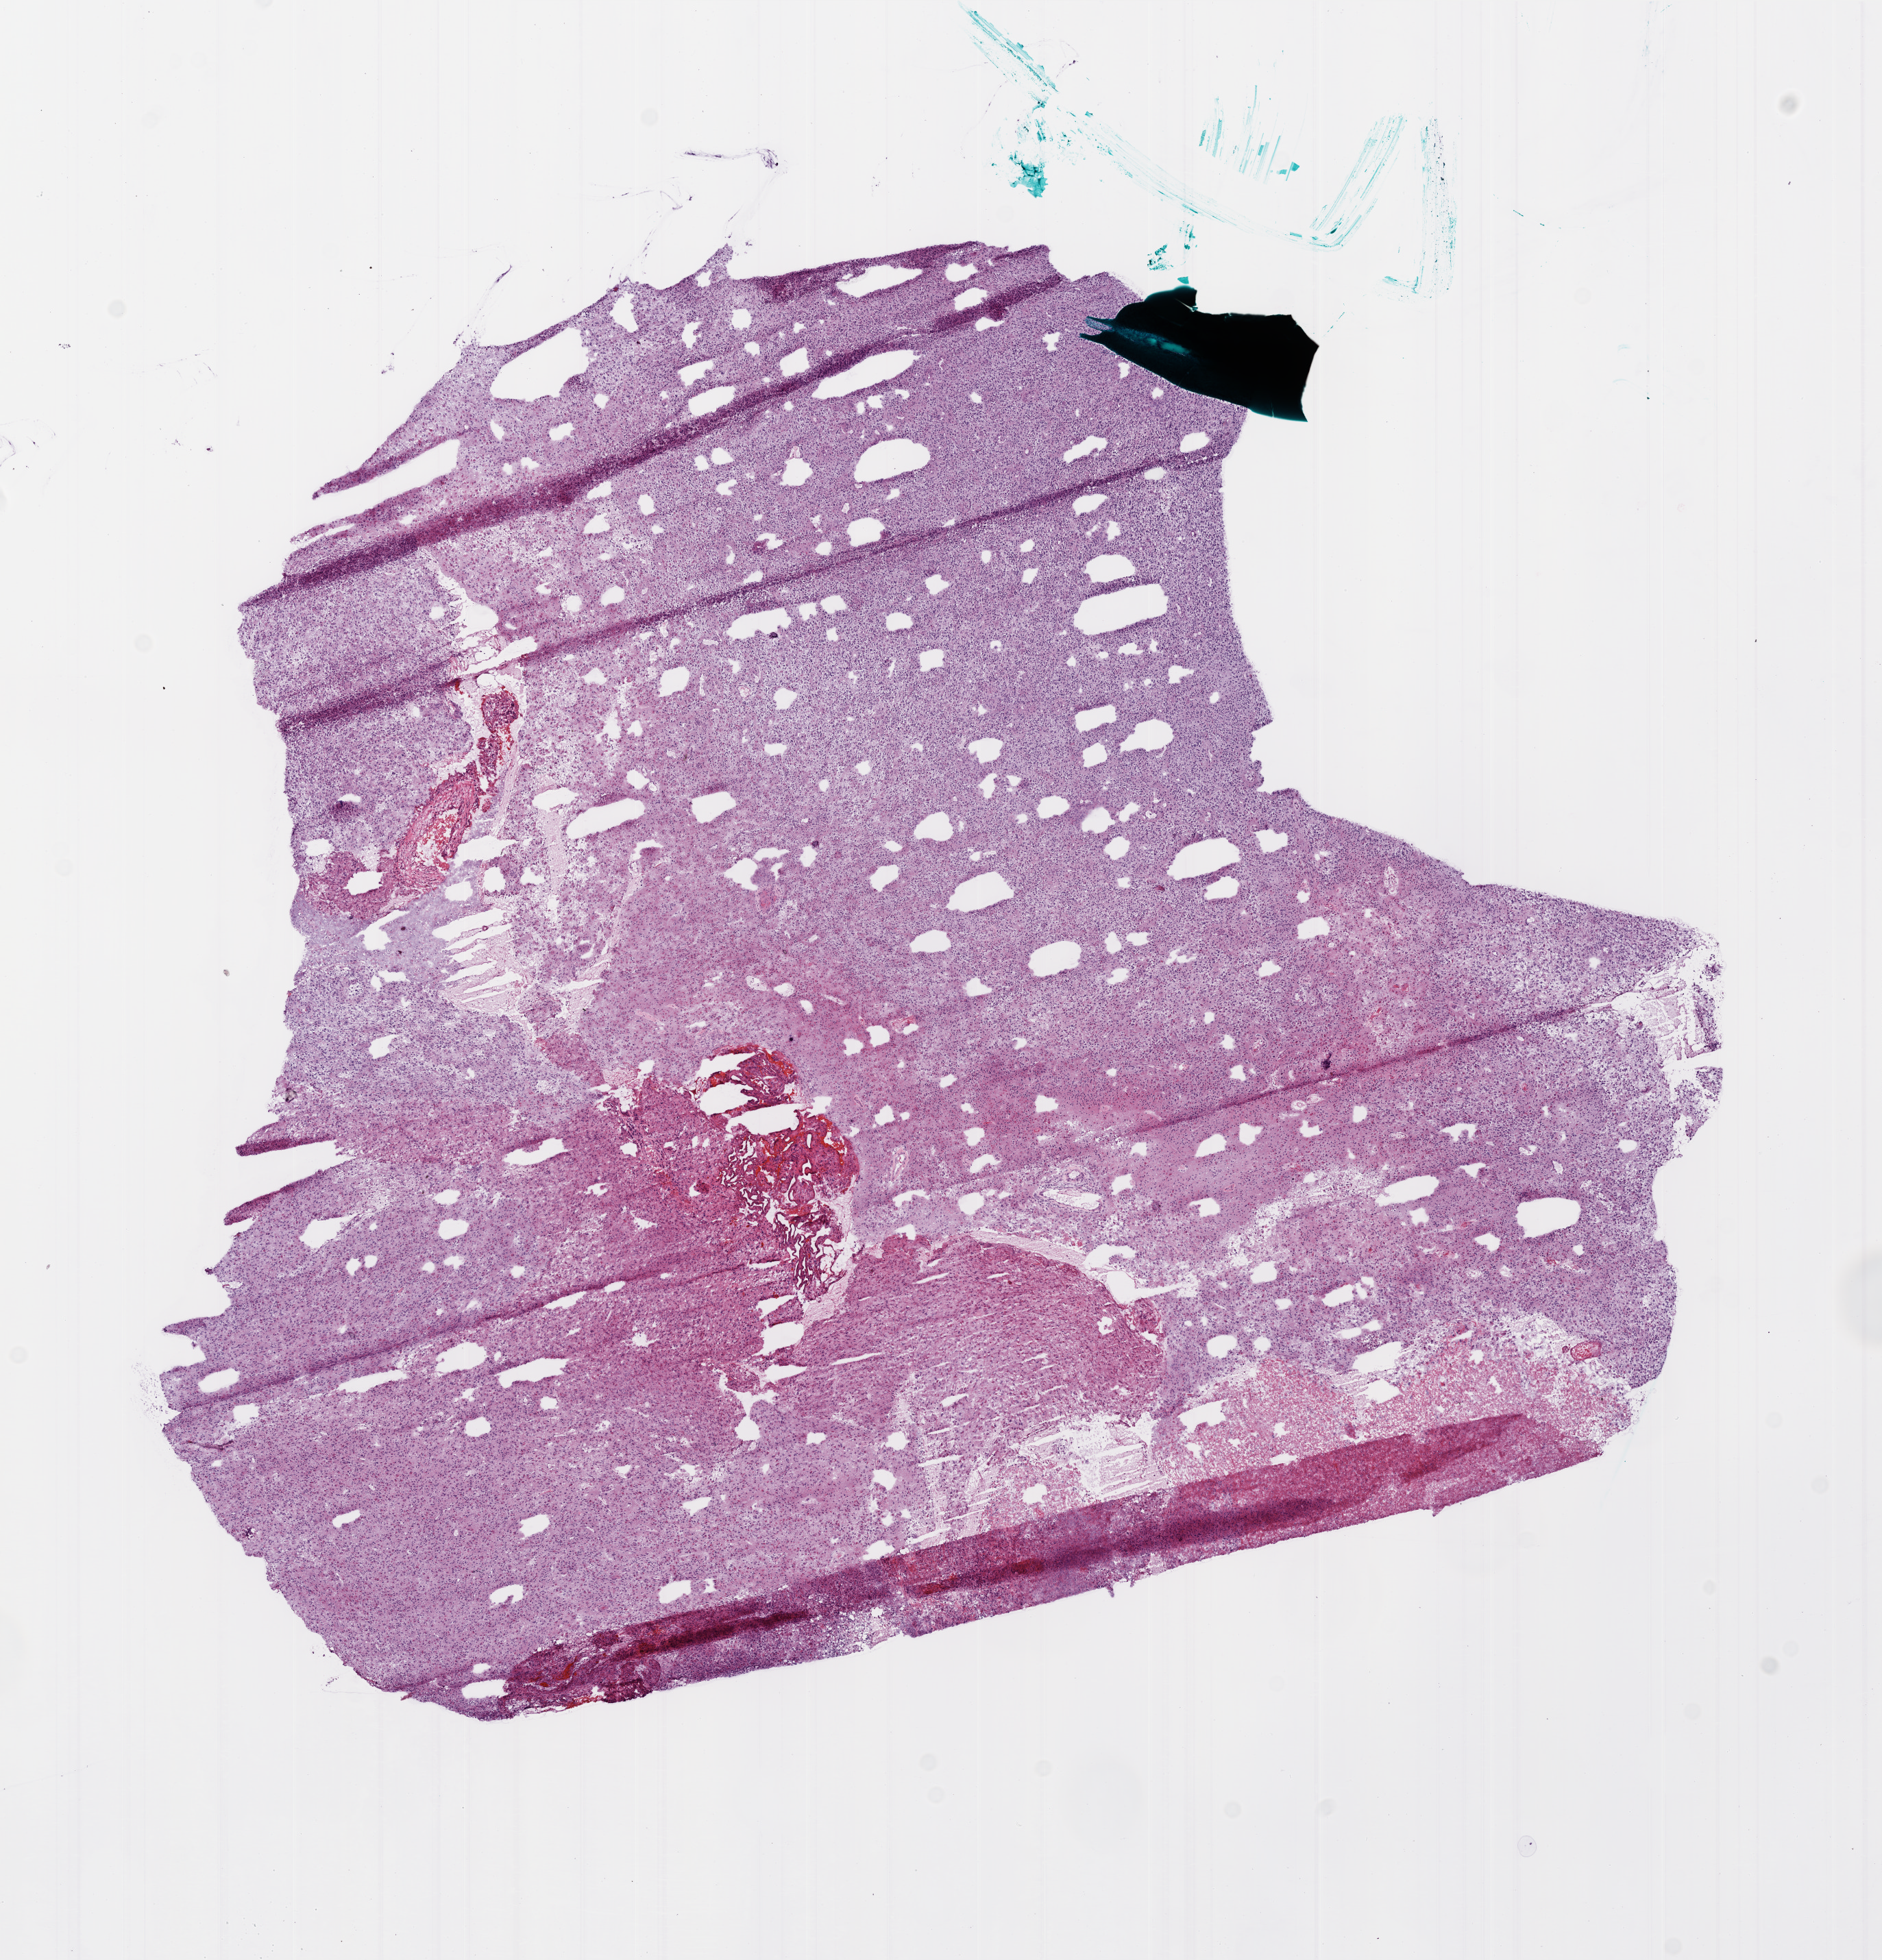
Whole-slide histology image, H&E — shown as a low-resolution overview of the whole scanned area (about 11.0 x 11.4 mm, acquisition: 20x scan). Frozen section. Brain, primary tumour sample. Patient: female, age at initial diagnosis 72 years. Slide review estimates, as recorded: tumour cells 95%, tumour nuclei 95%, normal cells 0%, stromal cells 0%, necrosis 5%.
* pathologic diagnosis: Glioblastoma